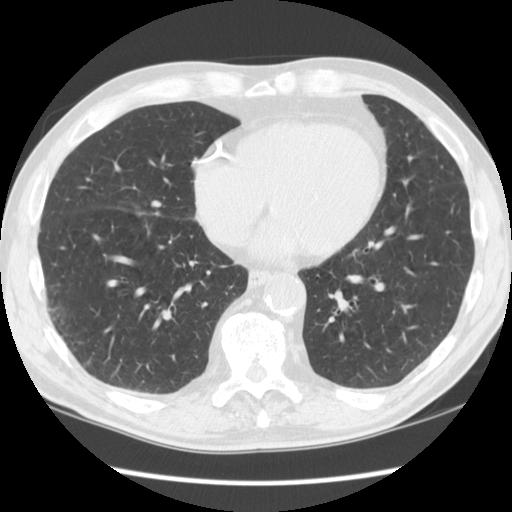
Low-dose screening chest CT, axial slice. Second screening round (one year after baseline). Lung window (W 1500 / L -600 HU). 2.5 mm slice thickness. Standard (soft-tissue) reconstruction kernel (STANDARD). 120 kVp. Male participant, aged 64 years at enrolment. Current smoker at enrolment.
- Expert-annotated lung lesion, bounding box [x1, y1, x2, y2] px = [128, 193, 175, 226].
- Screening reader's record for this exam (one nodule recorded; not confirmed to be the boxed lesion): non-calcified nodule or mass ≥4 mm, right middle lobe, 6 × 5 mm, smooth margins, soft tissue attenuation, pre-existing on the prior screen: no.